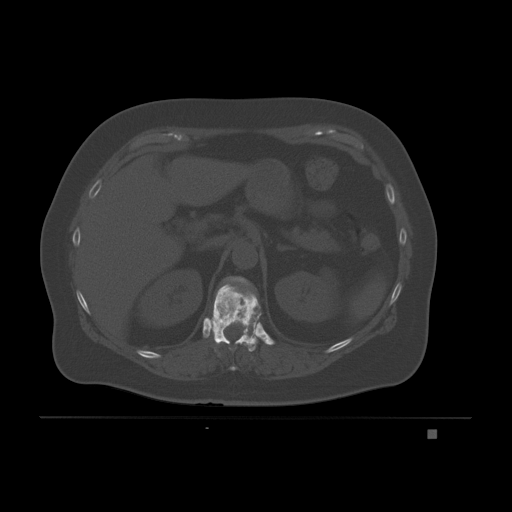
CT including the spine, one axial slice; position 91 of 221 along the scan axis; bone window (W 1800 / L 400 HU); 3 mm slice thickness; 512 × 512 image matrix, field of view 474 × 474 mm. Patient: female, 63 years. From the clinical record (not read from this slice): primary cancer: breast.
Structures marked on this image (semi-automatic segmentation, software-assisted and operator-edited):
- T10 vertebra: bounding box <228,347,252,371> (left, top, right, bottom; pixels)
- T11 vertebra: <212,283,262,351>
- T12 vertebra: <224,276,249,289>